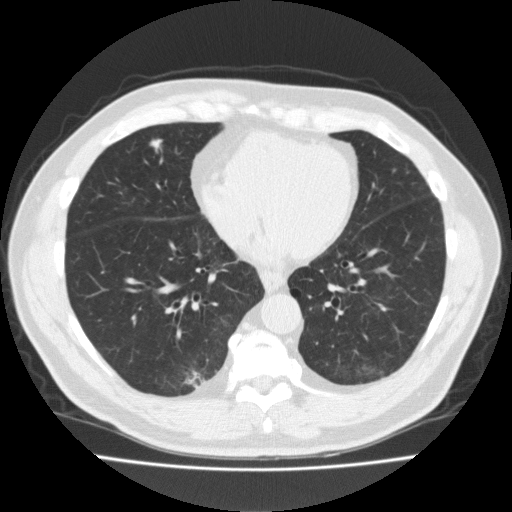
Low-dose screening chest CT, one axial slice. 120 kVp. Lung window (W 1500 / L -600 HU). 512 × 512 image matrix, field of view 369 × 369 mm.
Annotated regions visible in this slice (manually delineated by an expert):
- lesion 1 (tumor, middle lobe of right lung): bounding box (x1, y1, x2, y2) in pixels: (150, 139, 162, 152)